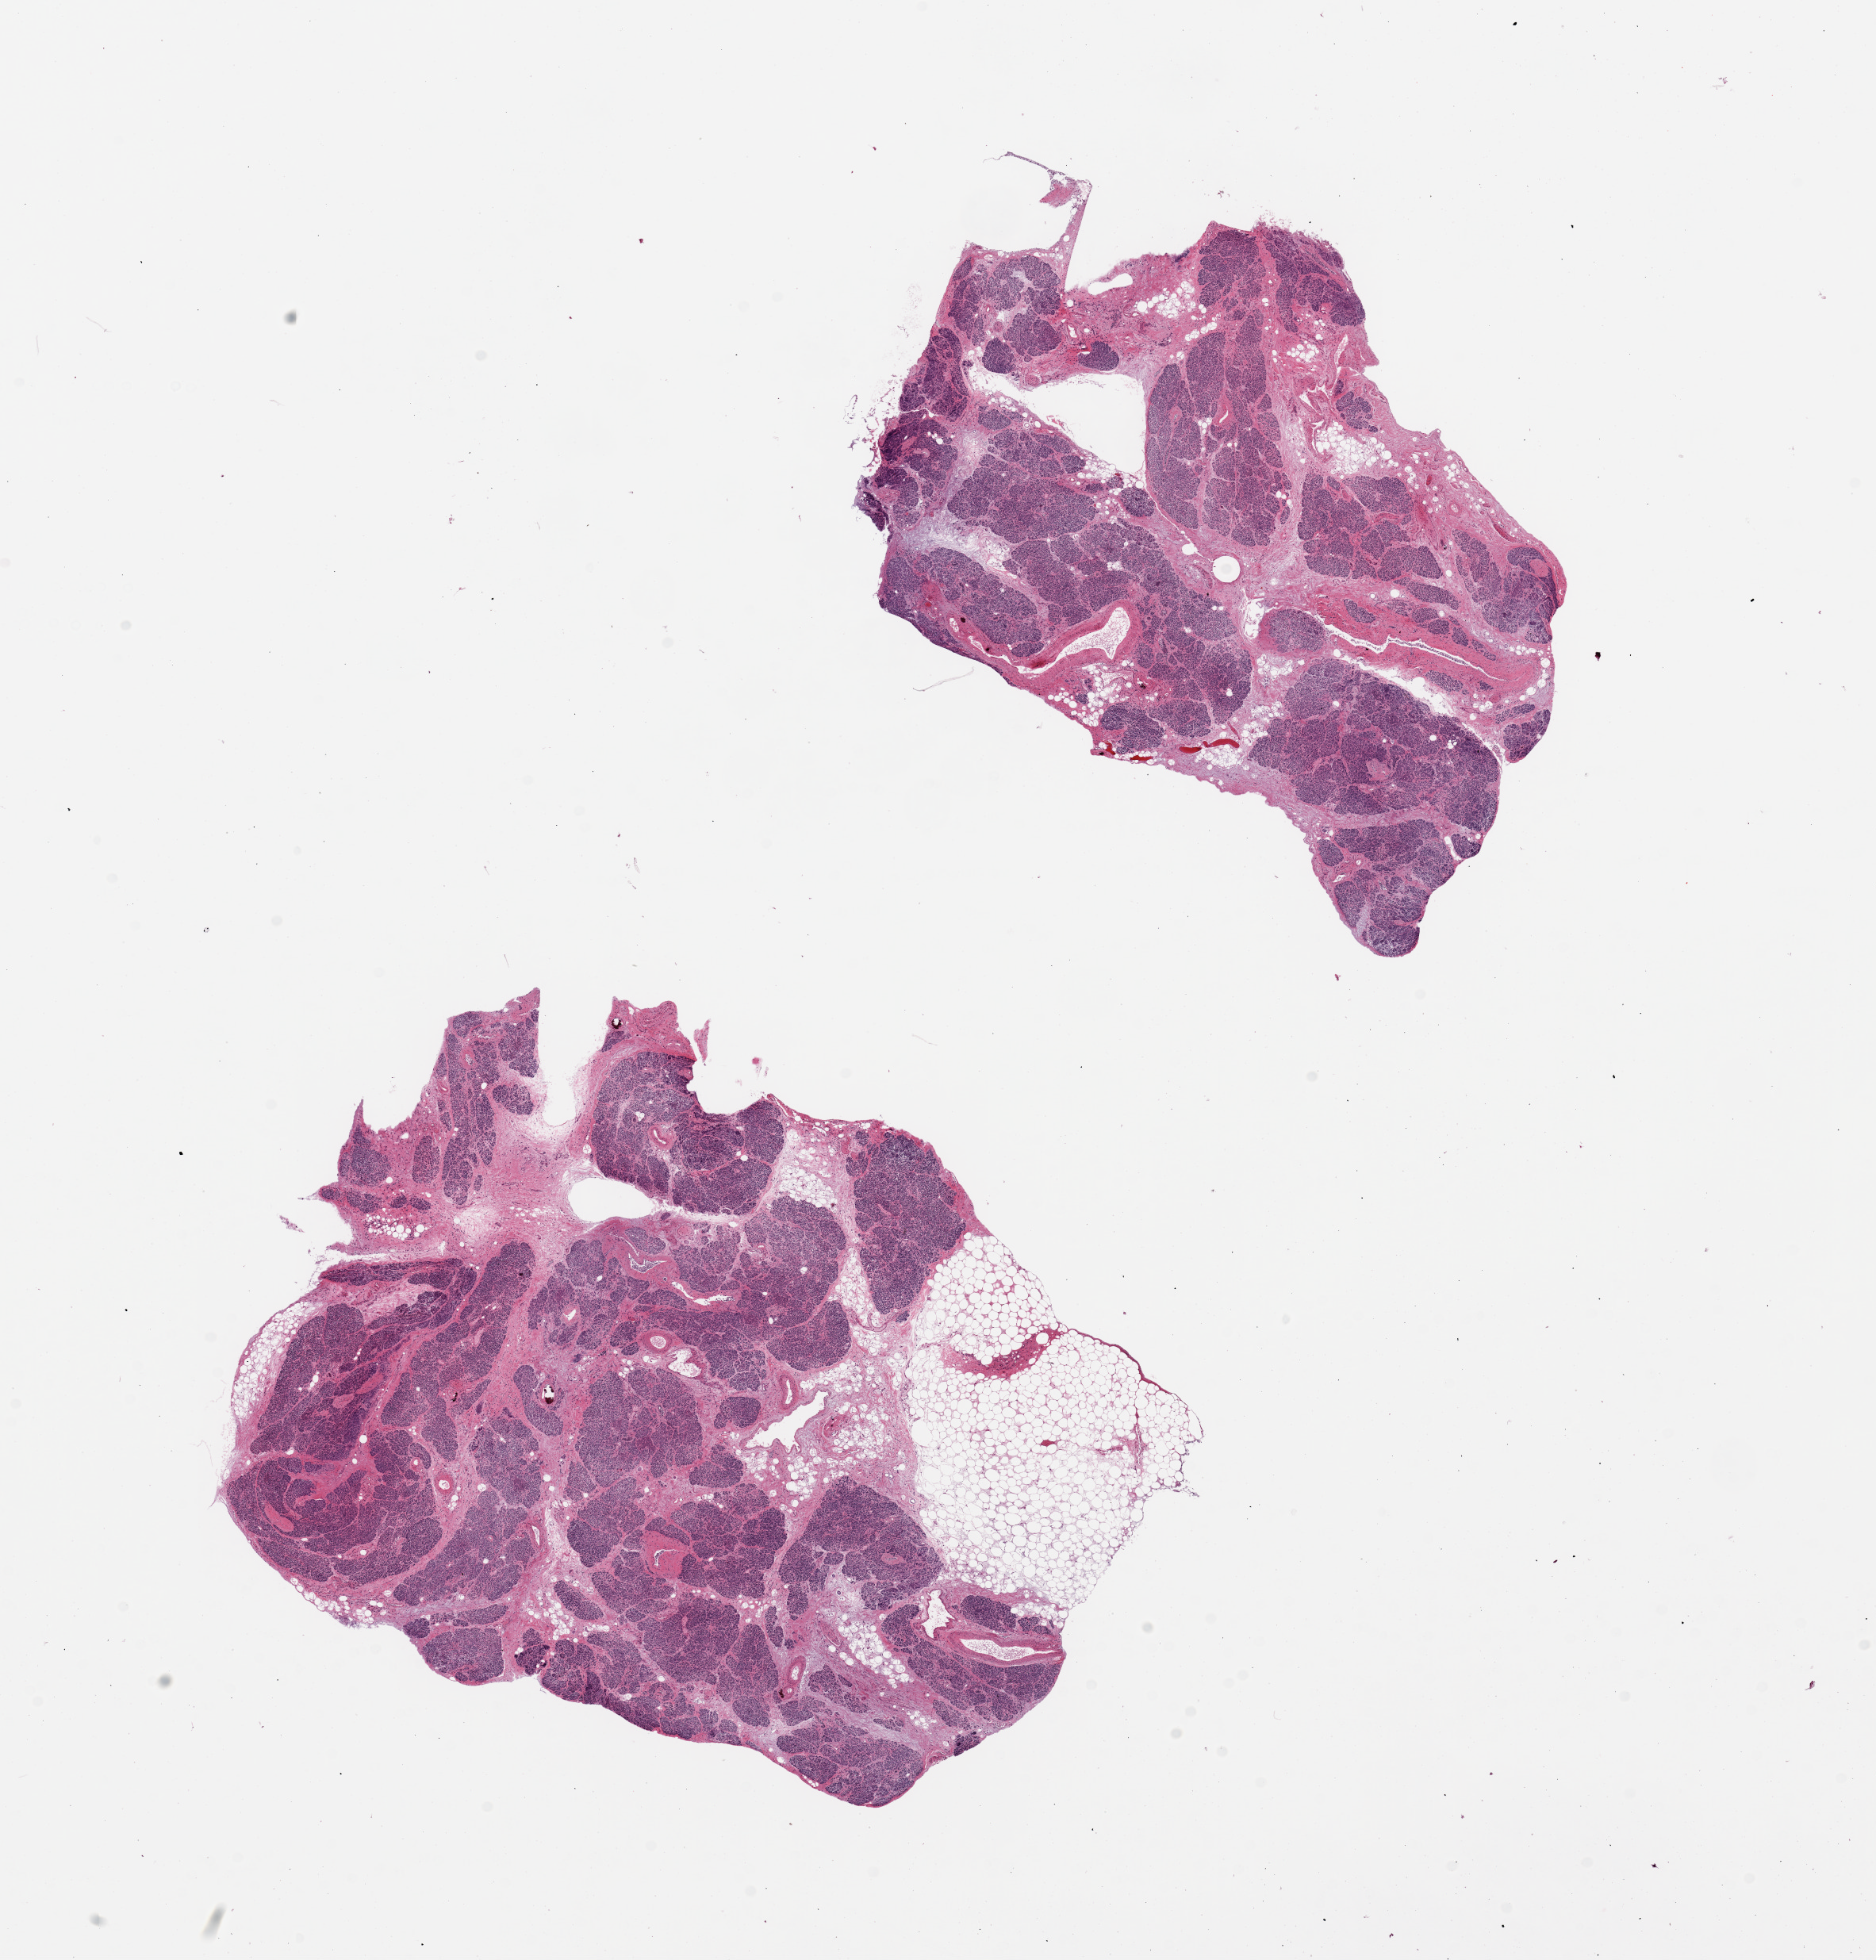
Whole-slide image, H&E stain — shown as a low-resolution overview of the whole scanned area (about 18.7 x 19.5 mm, acquisition: 20x scan). PAXgene-fixed paraffin-embedded (PFPE) section. Target tissue: pancreas. Donor tissue sample. Donor sex: female.
Reviewer comment on this tissue sample: 2 pieces, one piece includes ~20% fat, fibrosis.